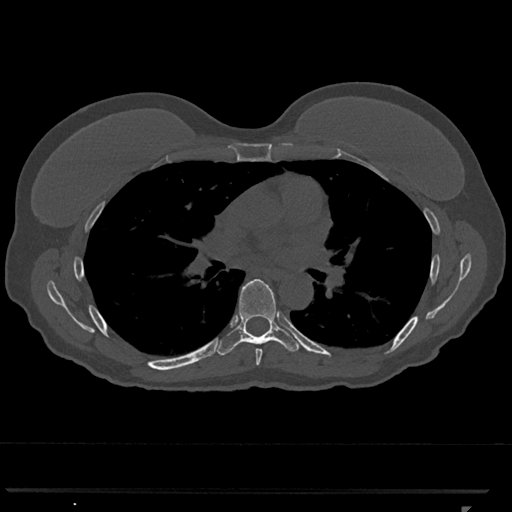
CT including the spine, one axial slice. Reconstruction kernel Br40s/3. Bone window (W 1800 / L 400 HU). 0.5 mm slice thickness. 512 × 512 image matrix. Patient: female, 62 years. Case-level facts recorded for this patient, not image findings: primary cancer: renal.
Annotated regions visible in this slice (semi-automatic segmentation, software-assisted and operator-edited):
- T6 vertebra: box from (x=255, y=349) to (x=263, y=365) px
- T7 vertebra: (x=216, y=279)–(x=300, y=356)